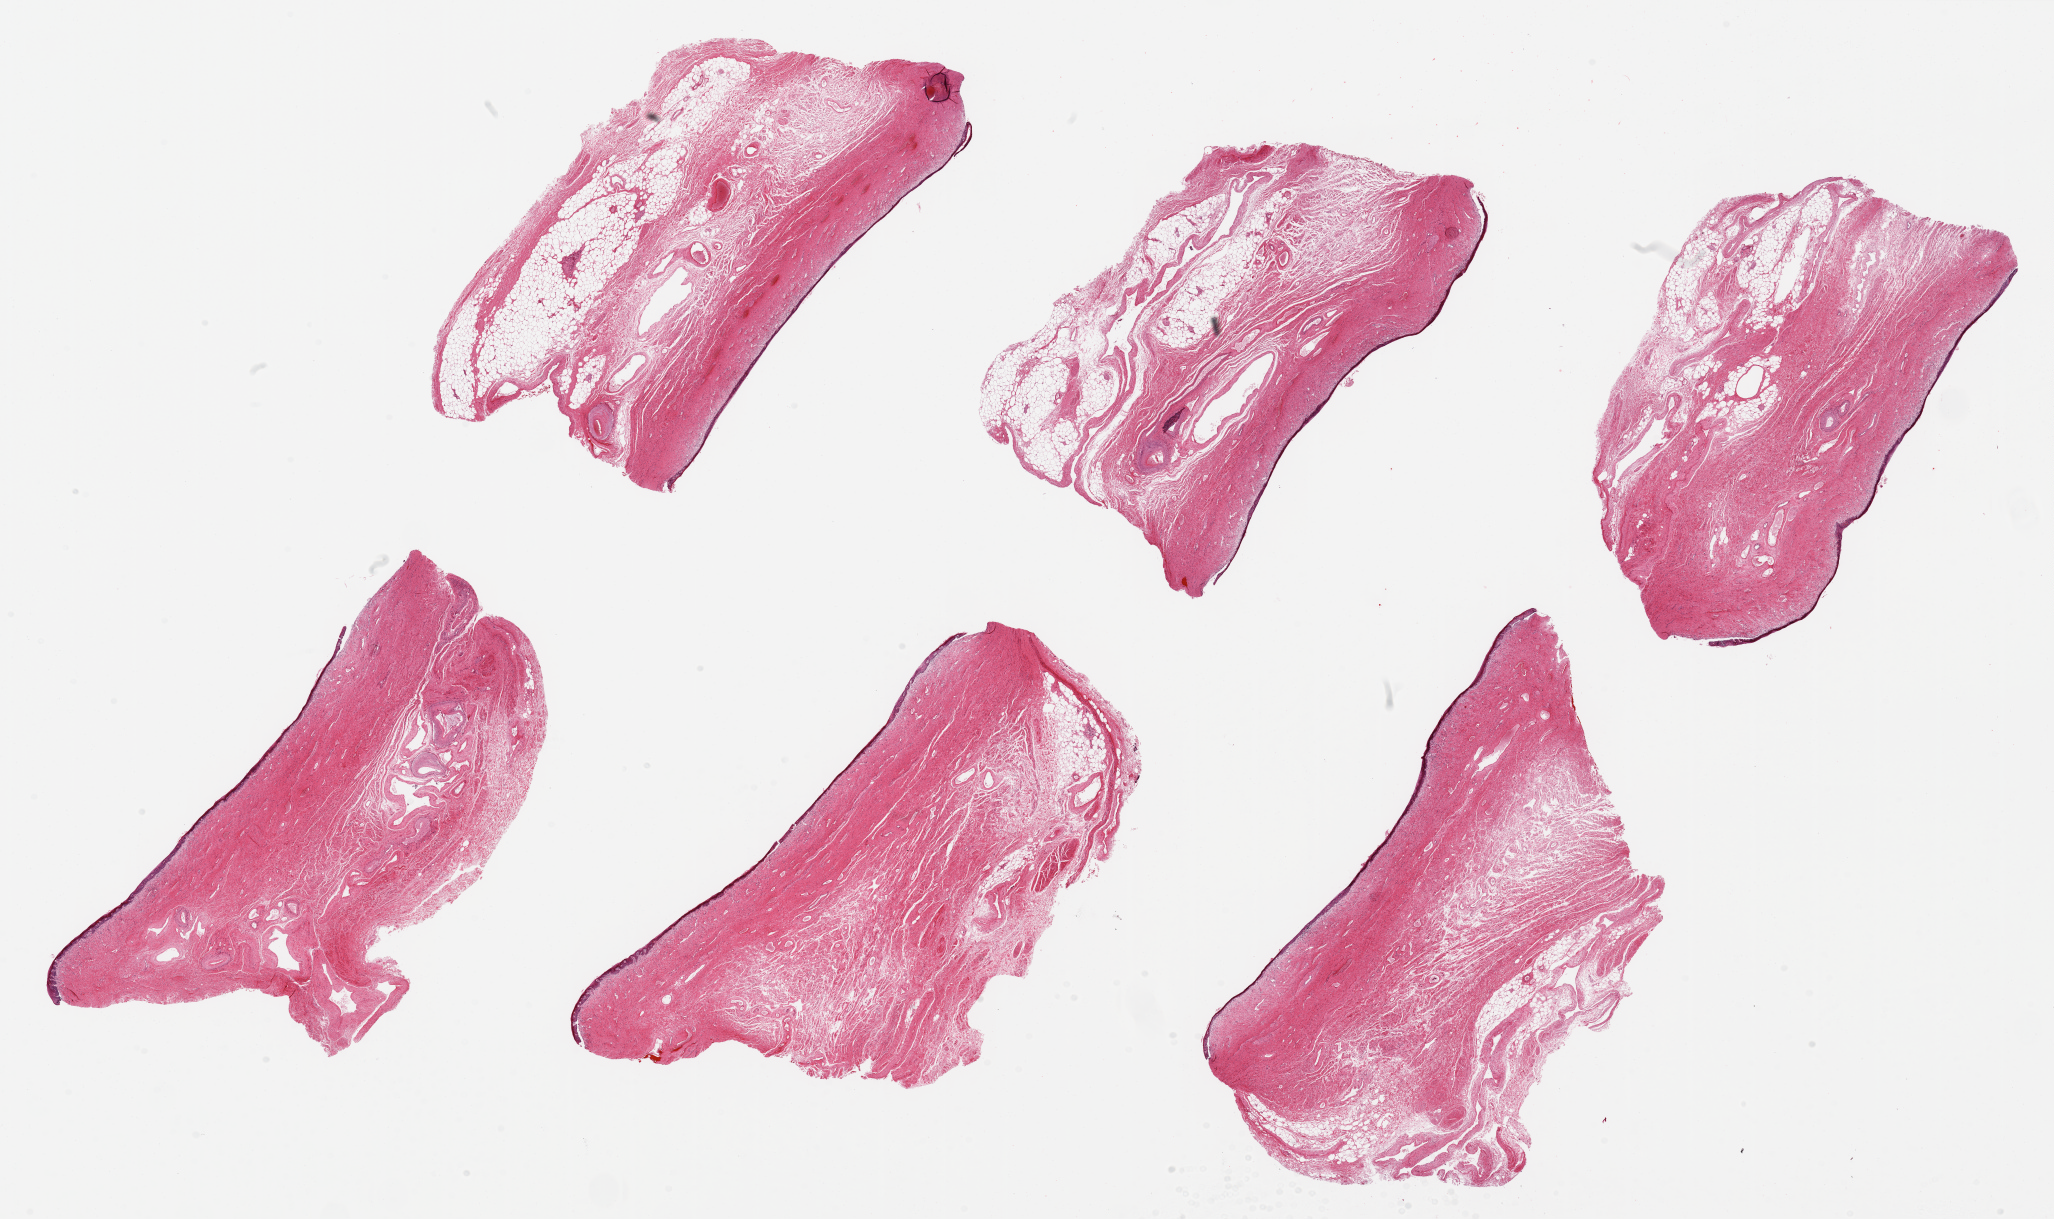
Whole-slide image, haematoxylin and eosin stain, a low-resolution overview of the entire scanned area, about 32.5 x 19.3 mm (slide scanned at 20x); PAXgene-fixed paraffin-embedded (PFPE) section; sampled site (target tissue): vagina; donor tissue sample.
* reviewer comment on this tissue sample: 6 ~8x4mm aliquots, deep fat present on most; squamous mucosa is ~1-2% of thickness, partially sloughing